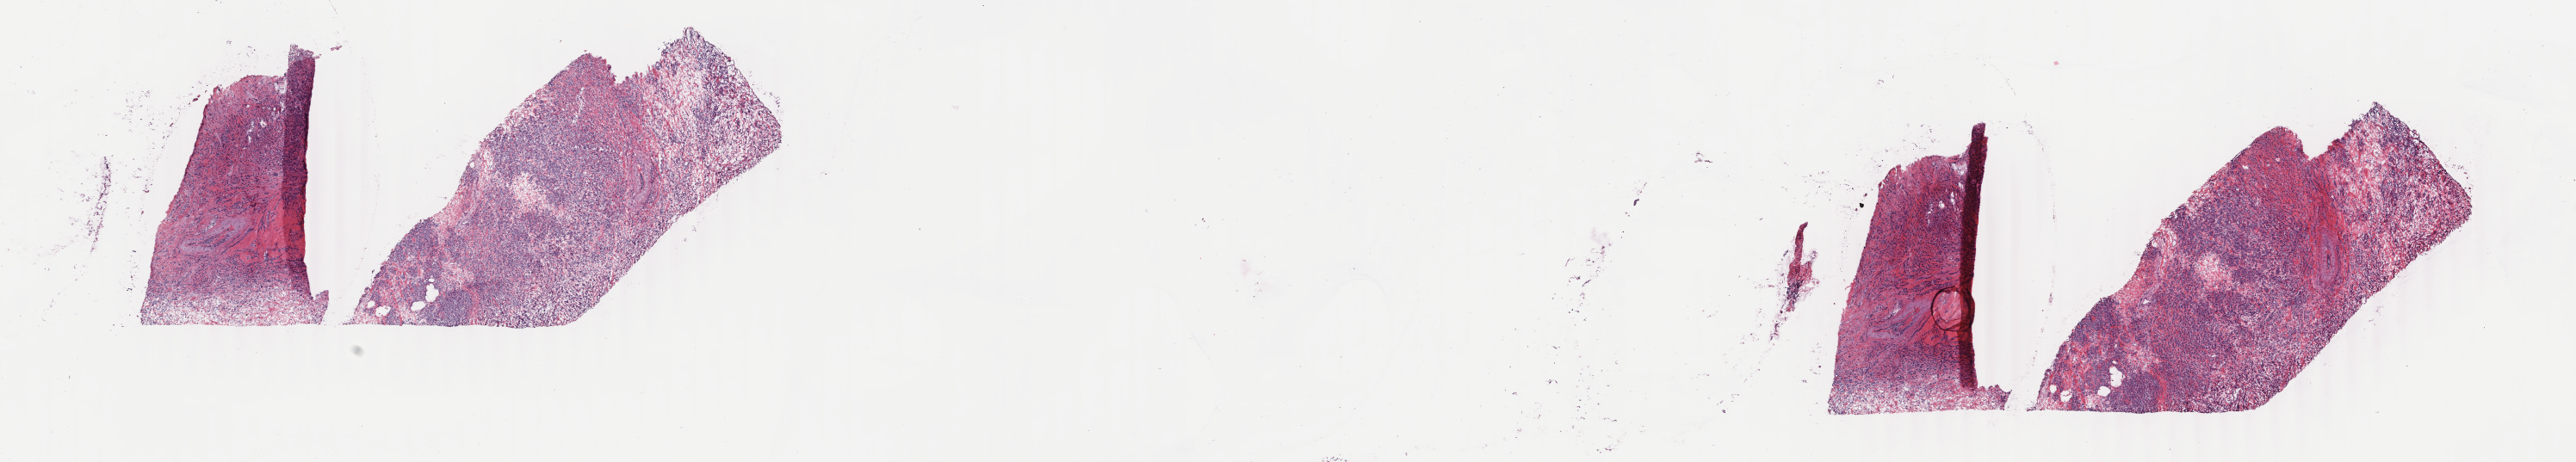
Digitized Hematoxylin and eosin (H&E) stained tissue section (whole slide) — whole scanned area (about 23.8 x 4.3 mm) shown as a low-resolution overview; frozen section; sample: primary tumour, breast. Female, age 73 years at initial diagnosis. Composition of this section per pathologist review: tumour cells 100%, tumour nuclei 85%, normal cells 0%, stromal cells 0%, necrosis 0%. Inflammatory infiltration, as recorded: lymphocyte infiltration 1%, monocyte infiltration 0%, neutrophil infiltration 0%.
Lymph nodes positive (case pathology): 3 of 26 examined. Laterality: right. AJCC pathologic stage: IIIA. Pathologic diagnosis: Lobular carcinoma, NOS.